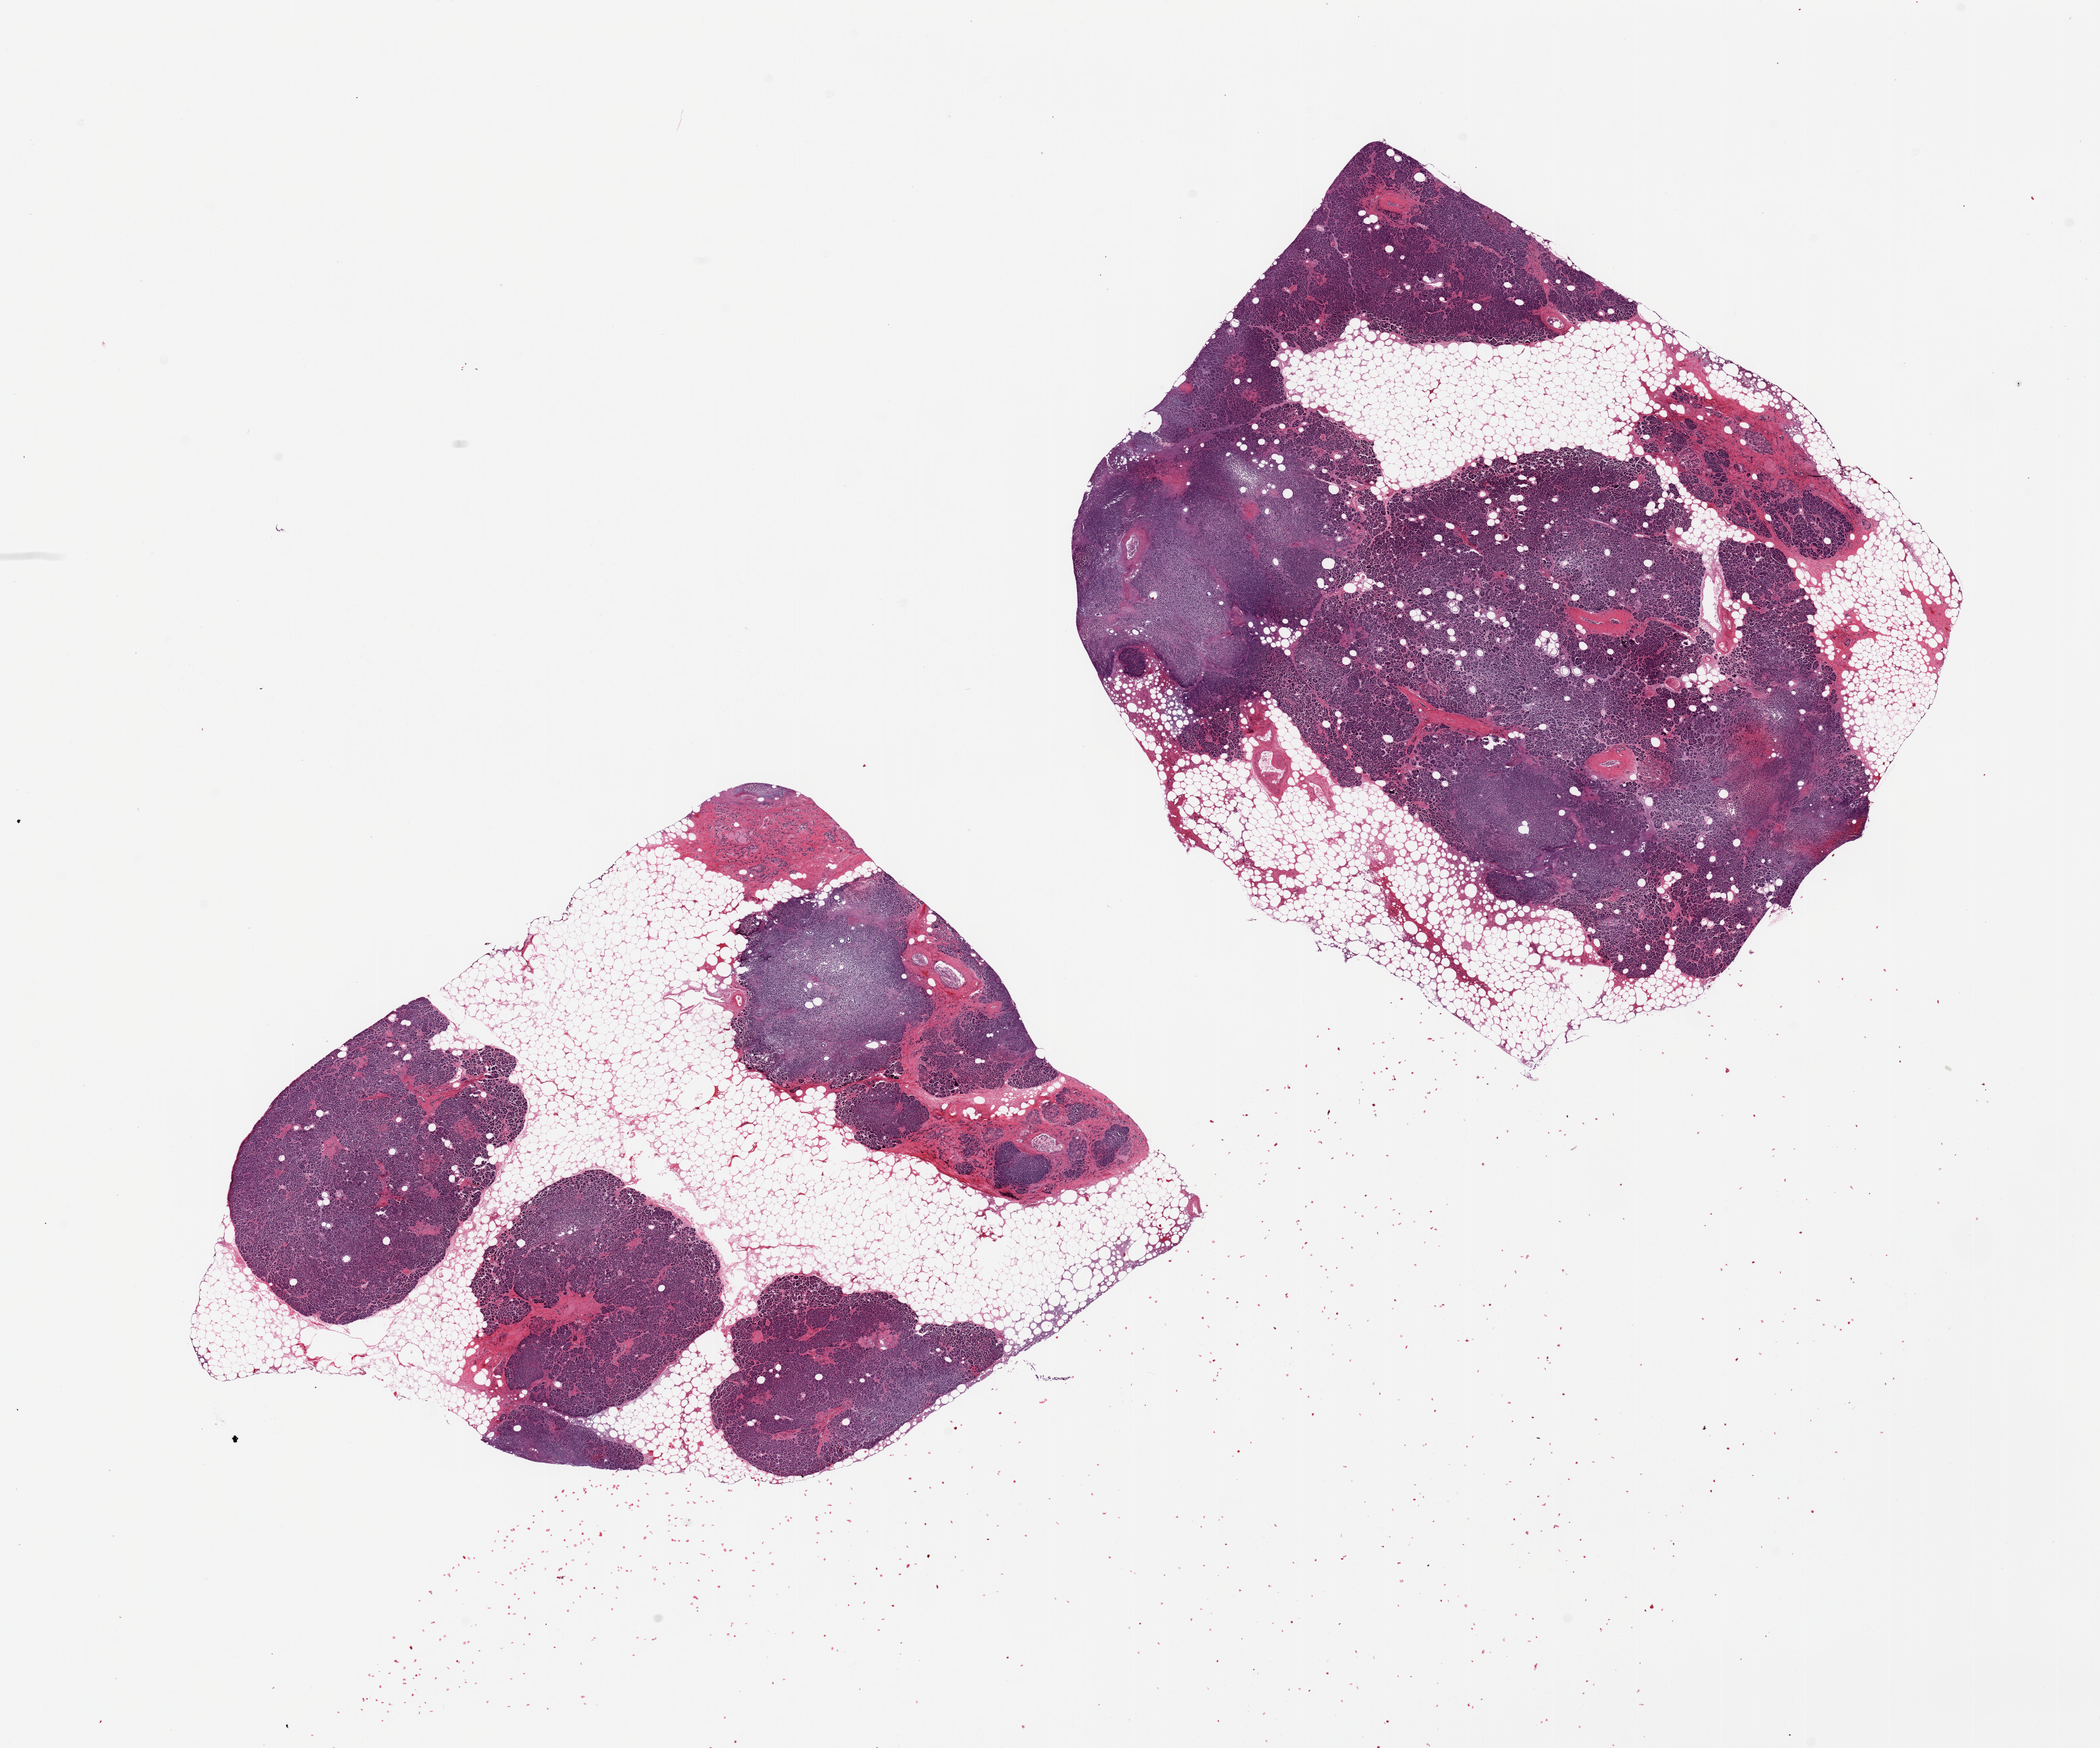
Digitized hematoxylin and eosin (H&E)-stained section, brightfield, shown as a low-resolution overview of the whole scanned area (about 24.6 x 20.5 mm), PAXgene-fixed, paraffin-embedded tissue, section of pancreas (target tissue), tissue donor sample.
Reviewer comment on this tissue sample: 2 pieces; 50 and 40% internal fat.